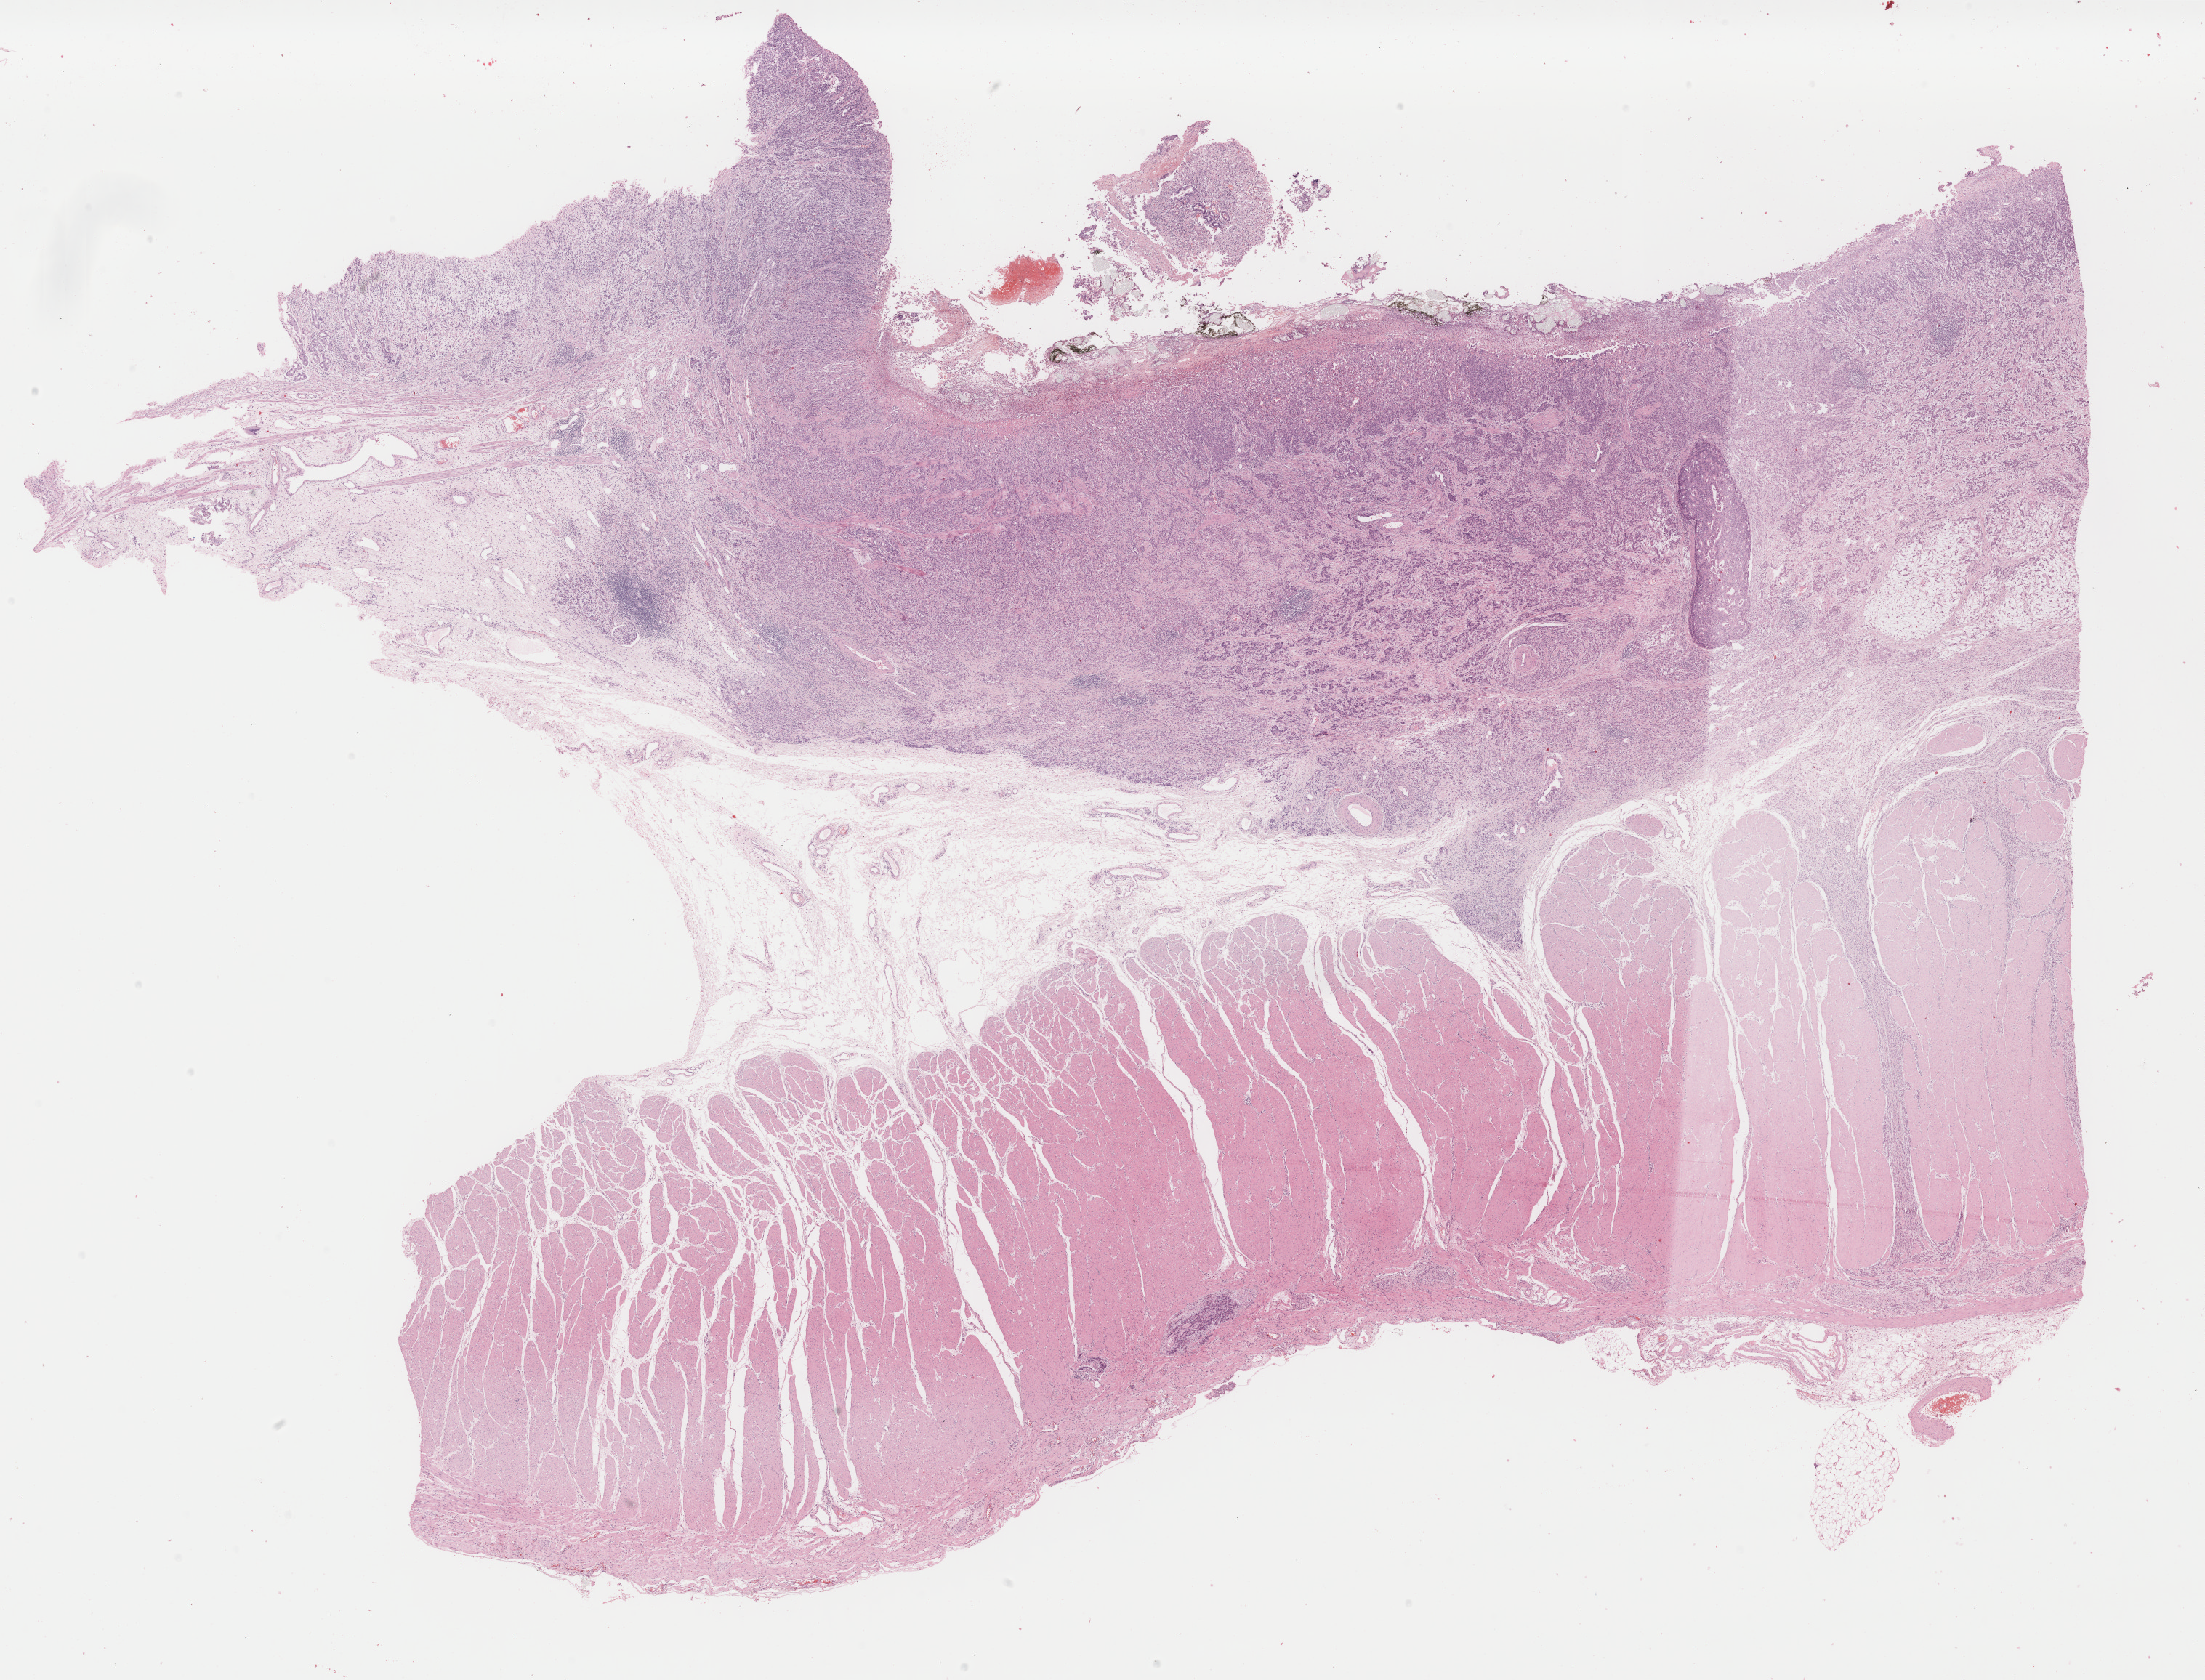
Whole-slide histology image, H&E-stained, low-resolution overview of the scanned area, about 24.1 x 18.4 mm (from a 40x scan); formalin-fixed paraffin-embedded (FFPE) diagnostic section; primary tumour sample from the stomach. Female, age 66 years at initial diagnosis.
Histologic diagnosis: Adenocarcinoma, intestinal type (gastric antrum).